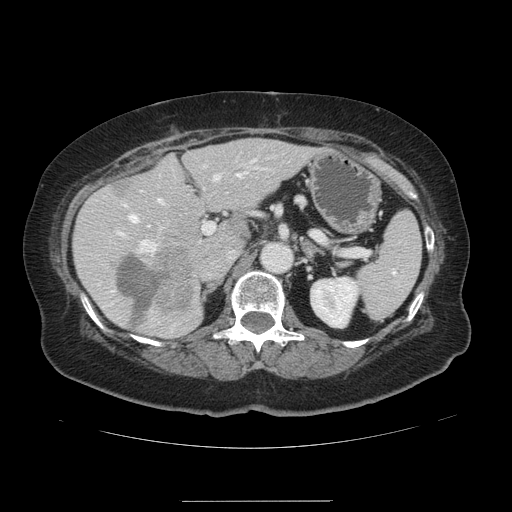
Contrast-enhanced abdominal CT, one axial slice. Slice 76 of 141 in the series (ordered by position). 120 kVp. Intravenous contrast given. Soft-tissue window (W 400 / L 40 HU). 512 × 512 image matrix, field of view 393 × 393 mm. Female patient, age 74 years. Case-level facts recorded for this patient, not image findings: diagnosis: colorectal cancer liver metastases, imaged before liver resection; multiple liver metastases: yes; largest metastasis: 7 cm; disease in both lobes: yes.
Outlined on this slice (outlined manually by an expert reader):
- hepatic veins: box from (x=129, y=173) to (x=240, y=227) px
- liver: (x=75, y=139)–(x=315, y=338)
- planned liver remnant (the part of the liver to remain after resection): (x=75, y=139)–(x=315, y=338)
- portal vein (with intrahepatic branches): (x=118, y=159)–(x=255, y=253)
- liver metastasis: (x=112, y=182)–(x=140, y=198)
- liver metastasis: (x=118, y=257)–(x=168, y=324)
- liver metastasis: (x=157, y=247)–(x=195, y=312)